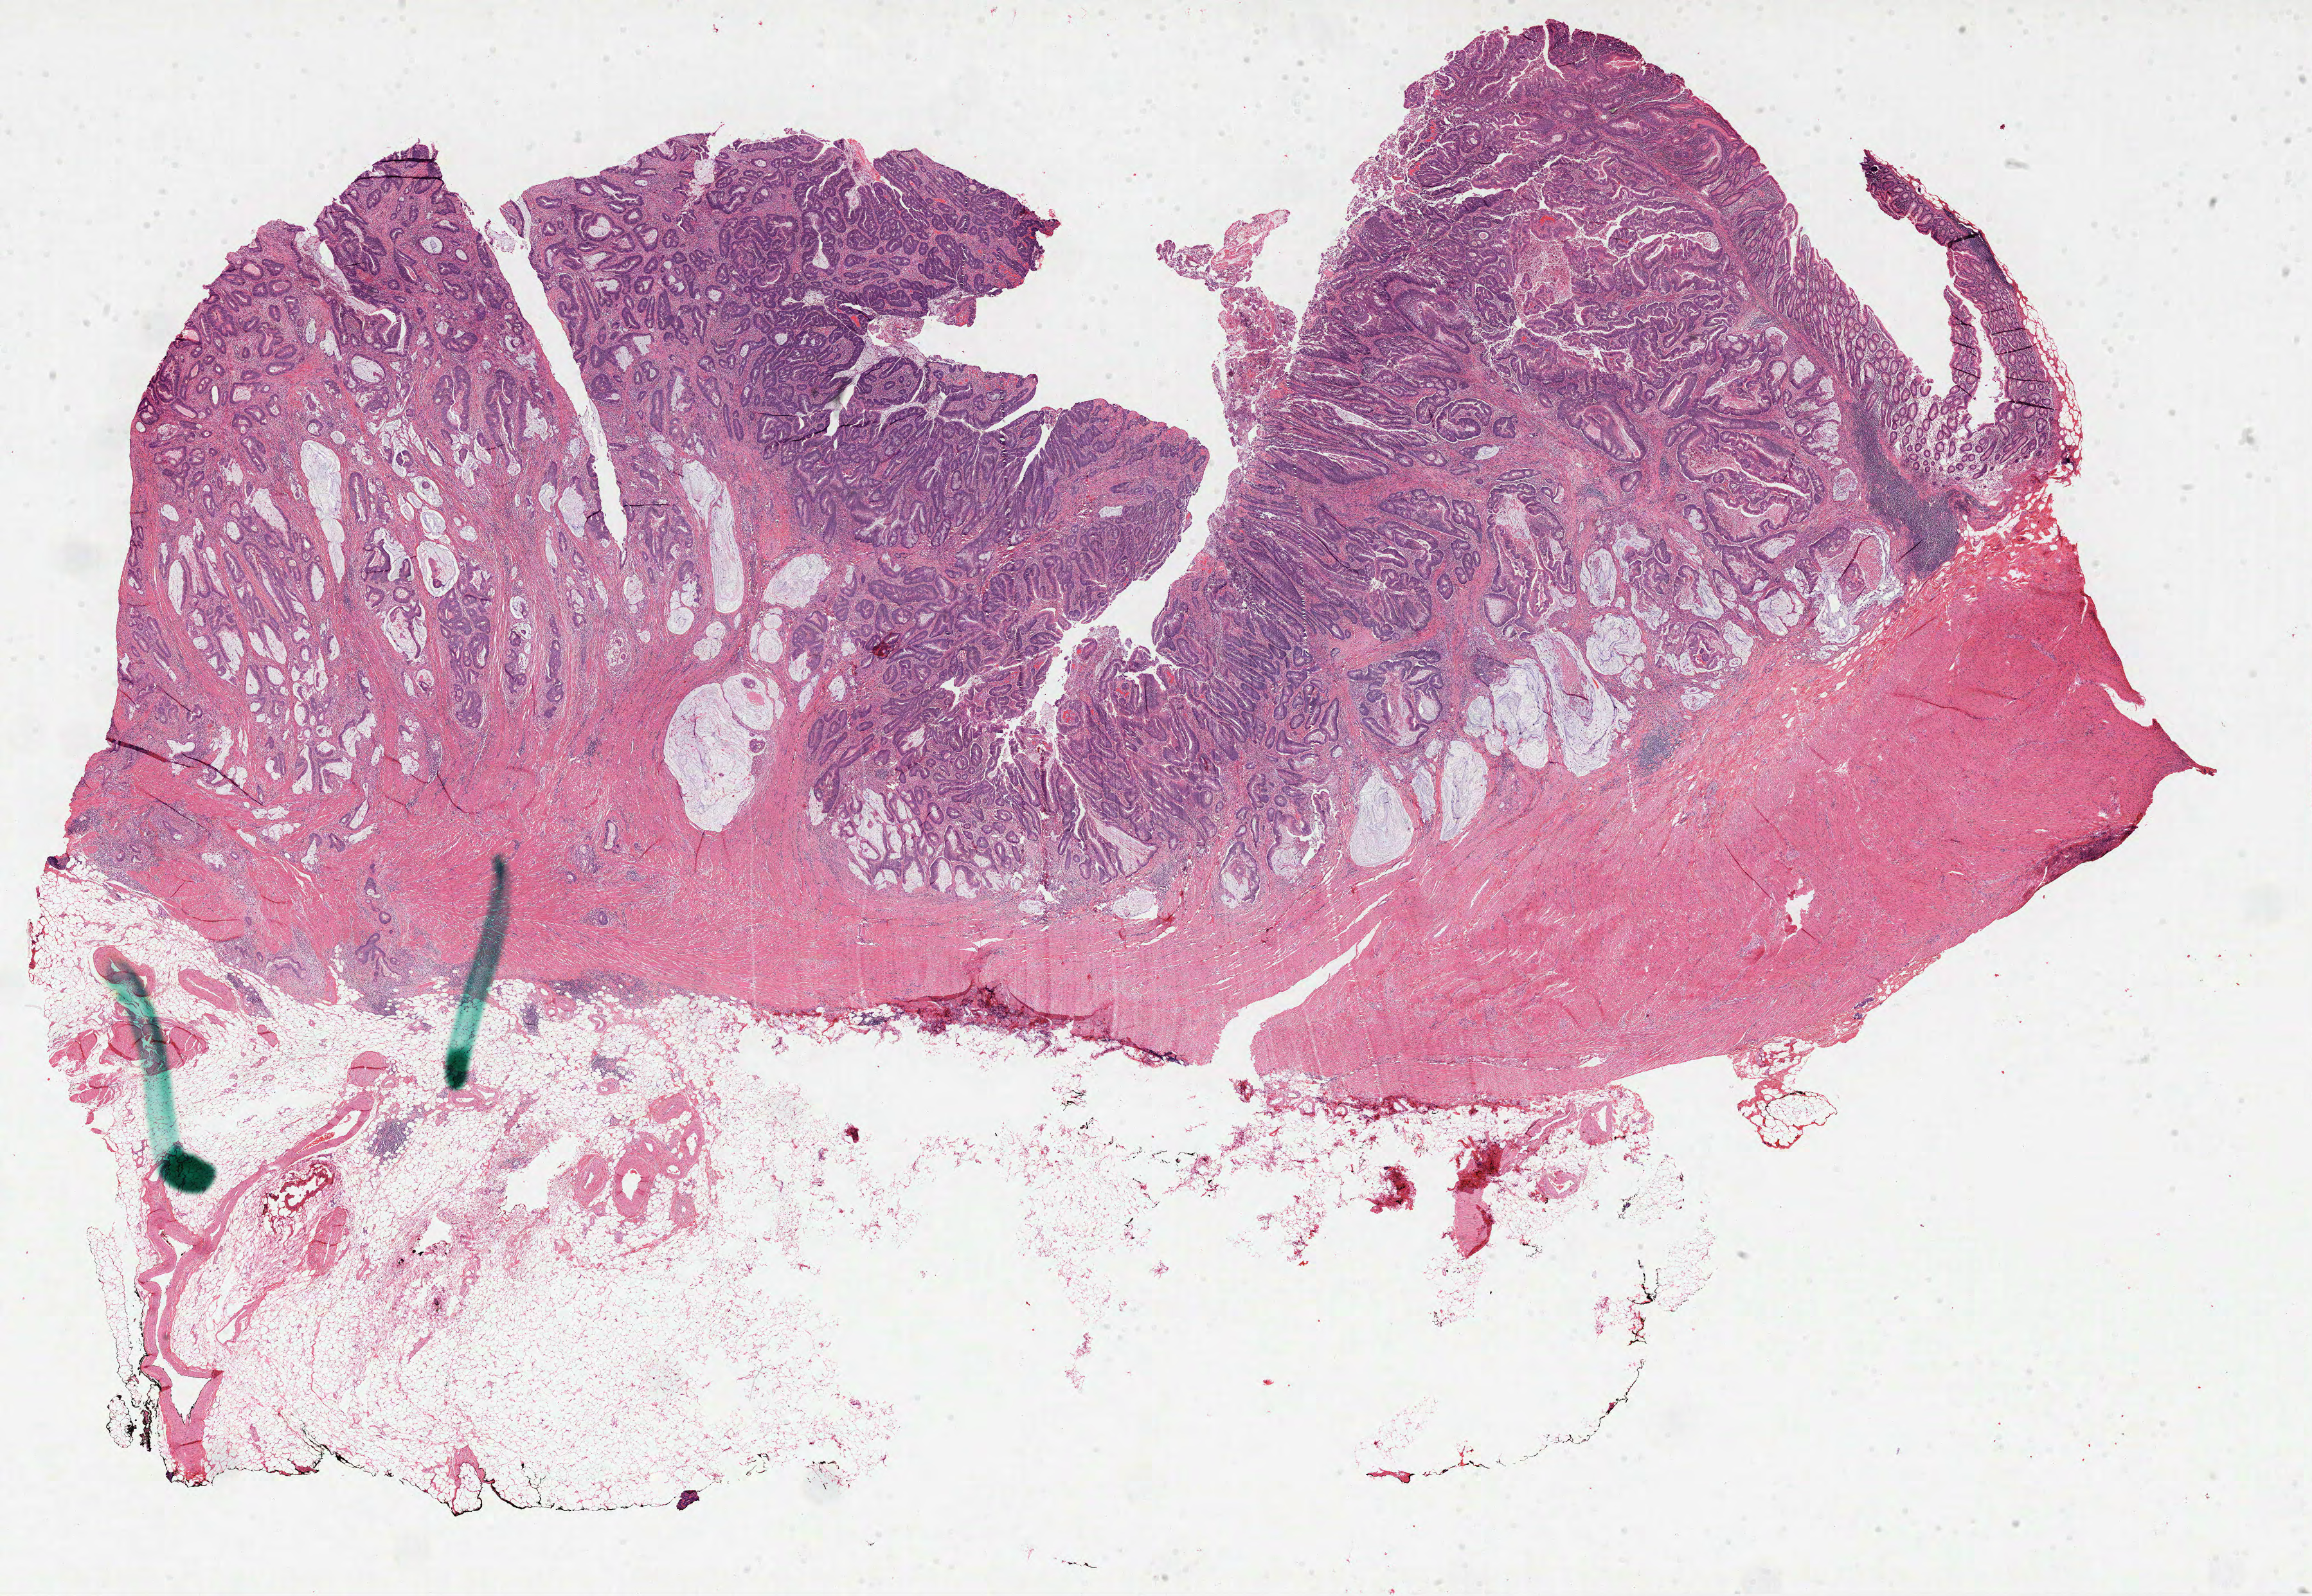
H&E whole-slide image, low-resolution overview of the scanned area, about 29.0 x 20.0 mm (from a 40x scan). Formalin-fixed paraffin-embedded (FFPE) diagnostic section. Colon, primary tumour sample. Female patient.
• AJCC pathologic stage: IIA (6th edition)
• histologic diagnosis: Adenocarcinoma, NOS (cecum)